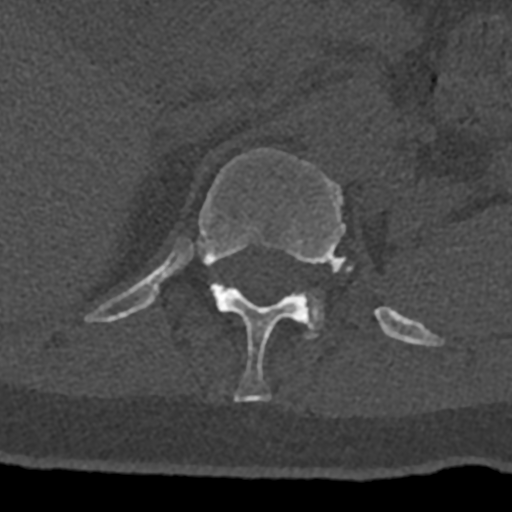
CT including the spine, one axial slice. Position 485 of 797 along the scan axis. Bone window (W 1800 / L 400 HU). 0.5 mm slice thickness. 512 × 512 image matrix, field of view 160 × 160 mm. Male patient, age 74 years. From the clinical record (not read from this slice): primary cancer: renal; vertebrae with lytic lesions (as recorded): T10, L1, L2, L3, L4, L5.
Structures marked on this image (semi-automatically segmented with operator editing):
- L1 vertebra: bounding box <306,293,324,338> (left, top, right, bottom; pixels)
- T12 vertebra: <85,149,432,402>